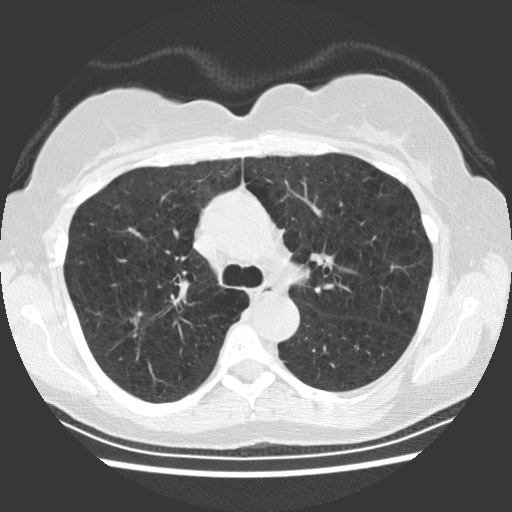
Low-dose screening chest CT, one axial slice. Slice 159 of 234 in the series (ordered by position). Reconstruction kernel STANDARD. Lung window (W 1500 / L -600 HU). 2.5 mm slice thickness. 512 × 512 image matrix.
Outlined on this slice (manually delineated by an expert):
- lesion 1 (tumor, upper lobe of right lung): bounding box <131,317,139,325> (left, top, right, bottom; pixels)